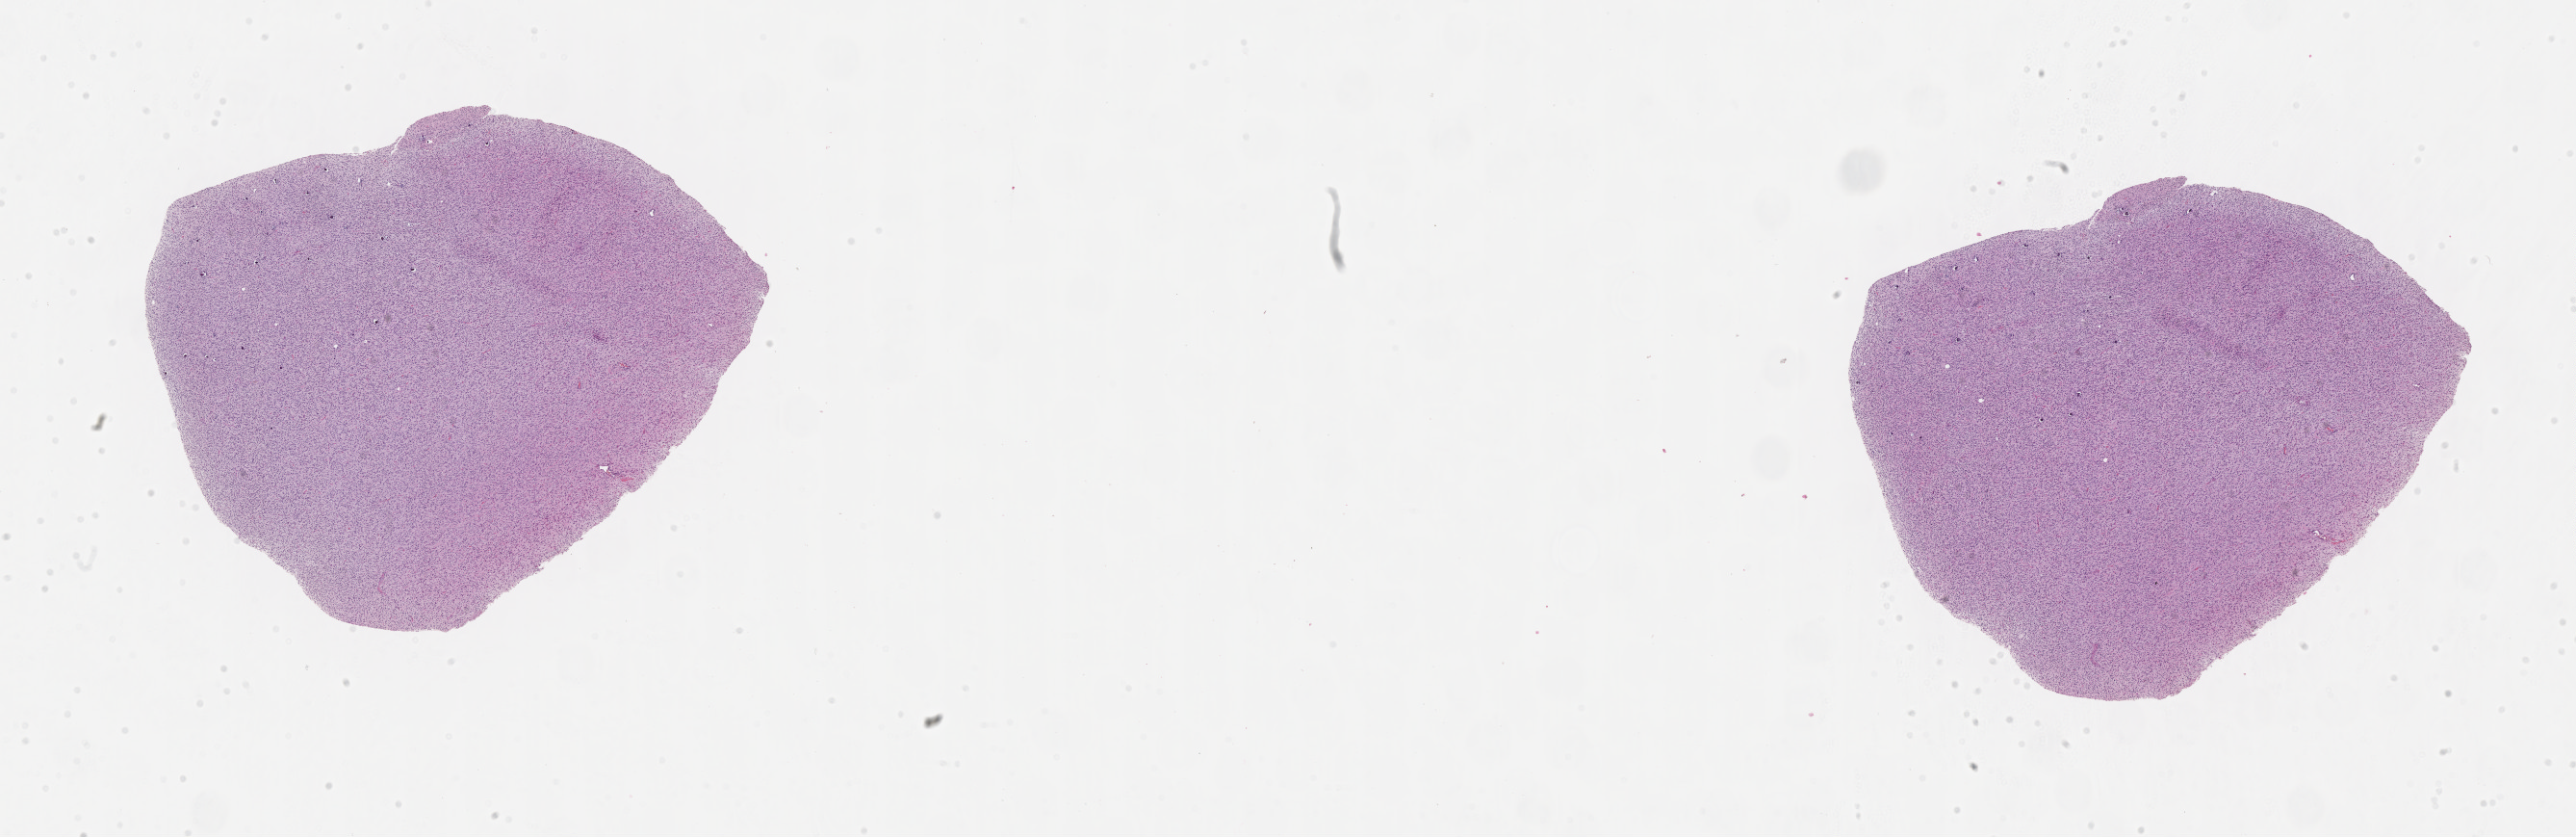
Whole-slide histology image, H&E-stained, shown as a low-resolution overview of the whole scanned area (about 21.6 x 7.0 mm); formalin-fixed paraffin-embedded (FFPE) diagnostic section; sample: primary tumour, brain. Male, age 55 years at initial diagnosis. Histologic grade: G3 (poorly differentiated).
Histologic diagnosis: Astrocytoma, anaplastic (cerebrum).